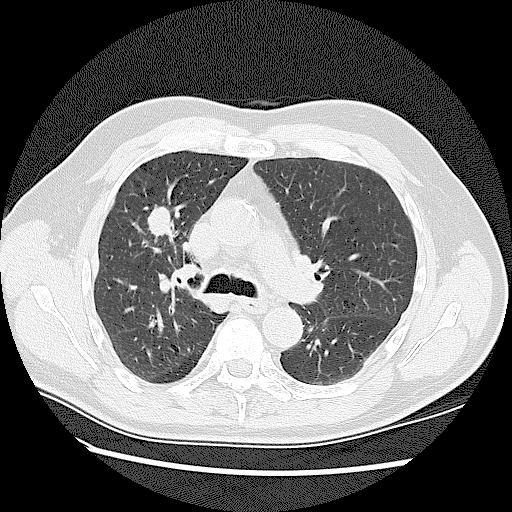
Low-dose screening chest CT, axial slice. Baseline annual screen. Lung window (W 1500 / L -600 HU). Lung (sharp) reconstruction kernel (LUNG). Male, age 72 years at enrolment.
Expert-annotated lung lesion, bounding box (x1, y1, x2, y2) in pixels: (133, 199, 181, 238). The screening reader recorded 2 non-calcified nodules or masses ≥4 mm on this exam (right upper lobe, right upper lobe); which of them this box marks is not recorded. Lung cancer was diagnosed 42 days after this screen: adenocarcinoma, NOS, right upper lobe, stage IV (AJCC 6th edition), 45 mm at pathology.